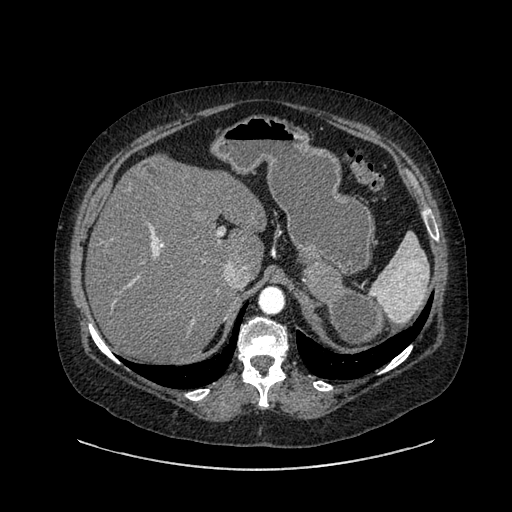
Contrast-enhanced abdominal CT, one axial slice. Slice 624 of 769 in the series (ordered by position). Reconstruction kernel SOFT. Intravenous contrast given. Soft-tissue window (W 400 / L 40 HU). 0.62 mm slice thickness. 512 × 512 image matrix, field of view 460 × 460 mm. Female patient, age 61 years. Case-level facts recorded for this patient, not image findings: diagnosis: adrenocortical carcinoma; tumour side: left adrenal; tumour size at pathology: 13 cm; Ki-67 index: 79 %; stage (as recorded): 2.
Structures marked on this image (semi-automatic segmentation, software-assisted and operator-edited):
- mass: bounding box <301,262,384,346> (left, top, right, bottom; pixels)